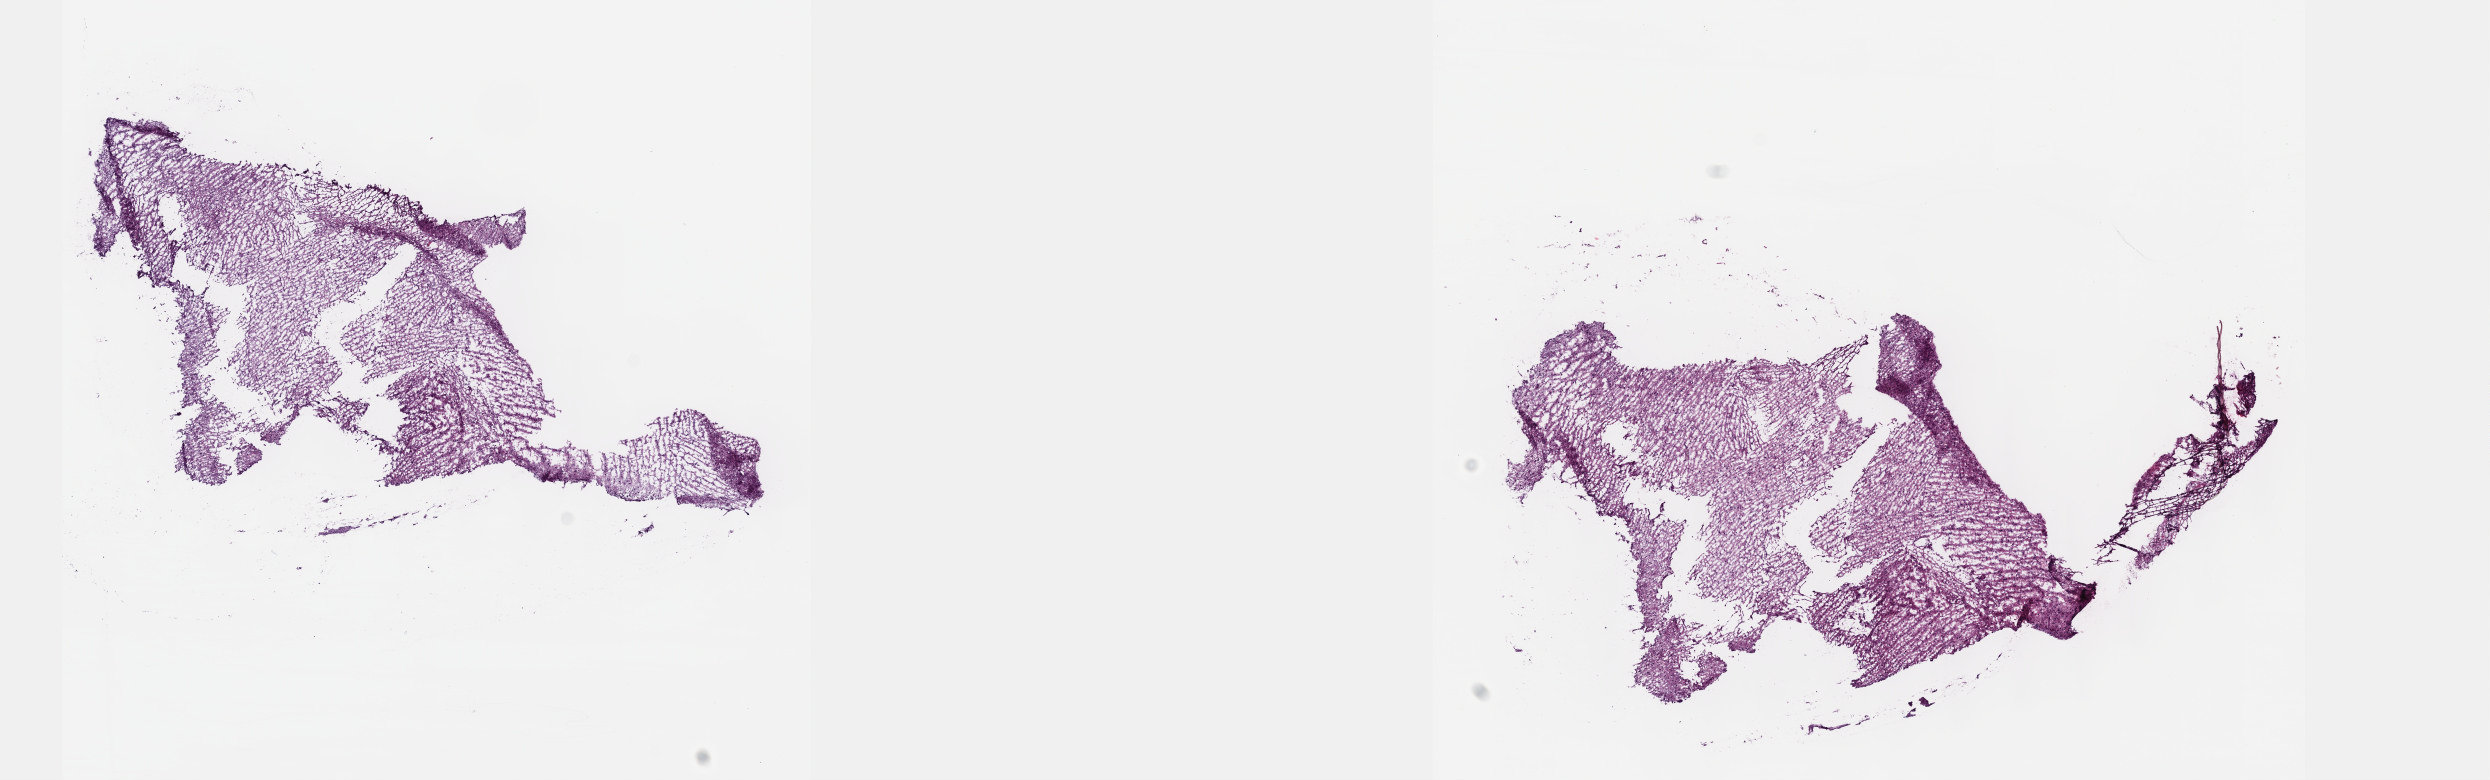
H&E whole-slide image, a low-resolution overview of the entire scanned area, about 20.1 x 6.3 mm (from a 40x scan); frozen section; primary tumour sample from the brain. Female patient; age at initial diagnosis 47 years. Histologic grade: G3 (poorly differentiated). Composition of this section per pathologist review: tumour cells 40%, tumour nuclei 90%, normal cells 10%, stromal cells 50%, necrosis 0%. Infiltration values recorded for this section: lymphocyte infiltration 0%, monocyte infiltration 0%, neutrophil infiltration 0%.
Histologic diagnosis: Astrocytoma, anaplastic (cerebrum).